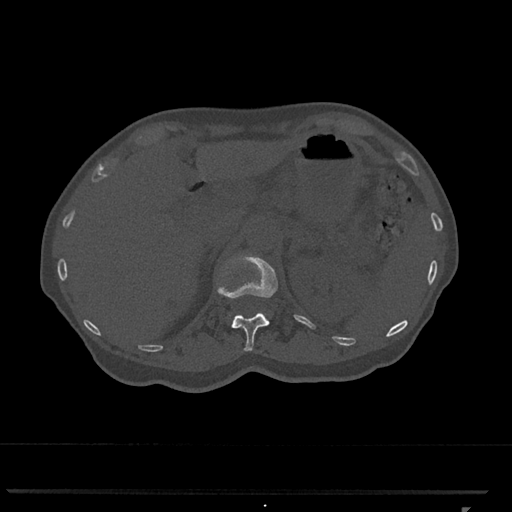
CT including the spine, one axial slice; position 446 of 793 along the scan axis; reconstruction kernel Br40s/3; bone window (W 1800 / L 400 HU); 0.5 mm slice thickness; 512 × 512 image matrix, field of view 380 × 380 mm. Female patient, age 62 years. Case-level facts recorded for this patient, not image findings: primary cancer: renal.
Structures marked on this image (semi-automatic segmentation, software-assisted and operator-edited):
- L1 vertebra: bounding box <249,255,254,257> (left, top, right, bottom; pixels)
- T12 vertebra: <217,255,278,351>